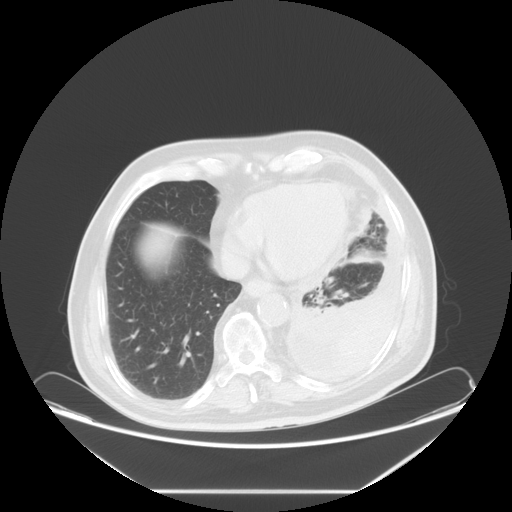
Chest CT, one axial slice; slice 21 of 63 in the series (ordered by position); reconstruction kernel STANDARD; lung window (W 1500 / L -600 HU); 5 mm slice thickness; 512 × 512 image matrix. Patient: male, 67 years. Case-level facts recorded for this patient, not image findings: clinical TNM (as recorded): T1b N1 M1a; histopathological grade: G3.
Outlined on this slice (rectangle marked by the reading radiologist):
- lung tumour (recorded histology: small cell carcinoma): box from (x=348, y=239) to (x=387, y=268) px